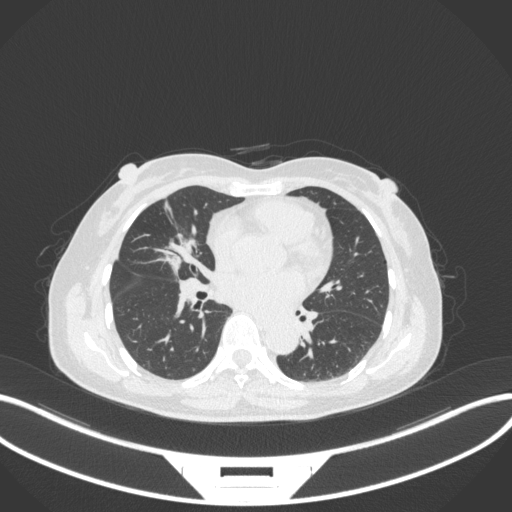
Chest CT, one axial slice. Slice 143 of 282 in the series (ordered by position). Reconstruction kernel B31f. 120 kVp. Lung window (W 1500 / L -600 HU). 1 mm slice thickness. 512 × 512 image matrix, field of view 400 × 400 mm. Patient: female, 51 years. Case-level facts recorded for this patient, not image findings: clinical TNM (as recorded): T1c N0 M0.
Outlined on this slice (bounding box drawn by a radiologist):
- lung tumour (recorded histology: adenocarcinoma): bounding box [x1, y1, x2, y2] px = [156, 227, 199, 276]